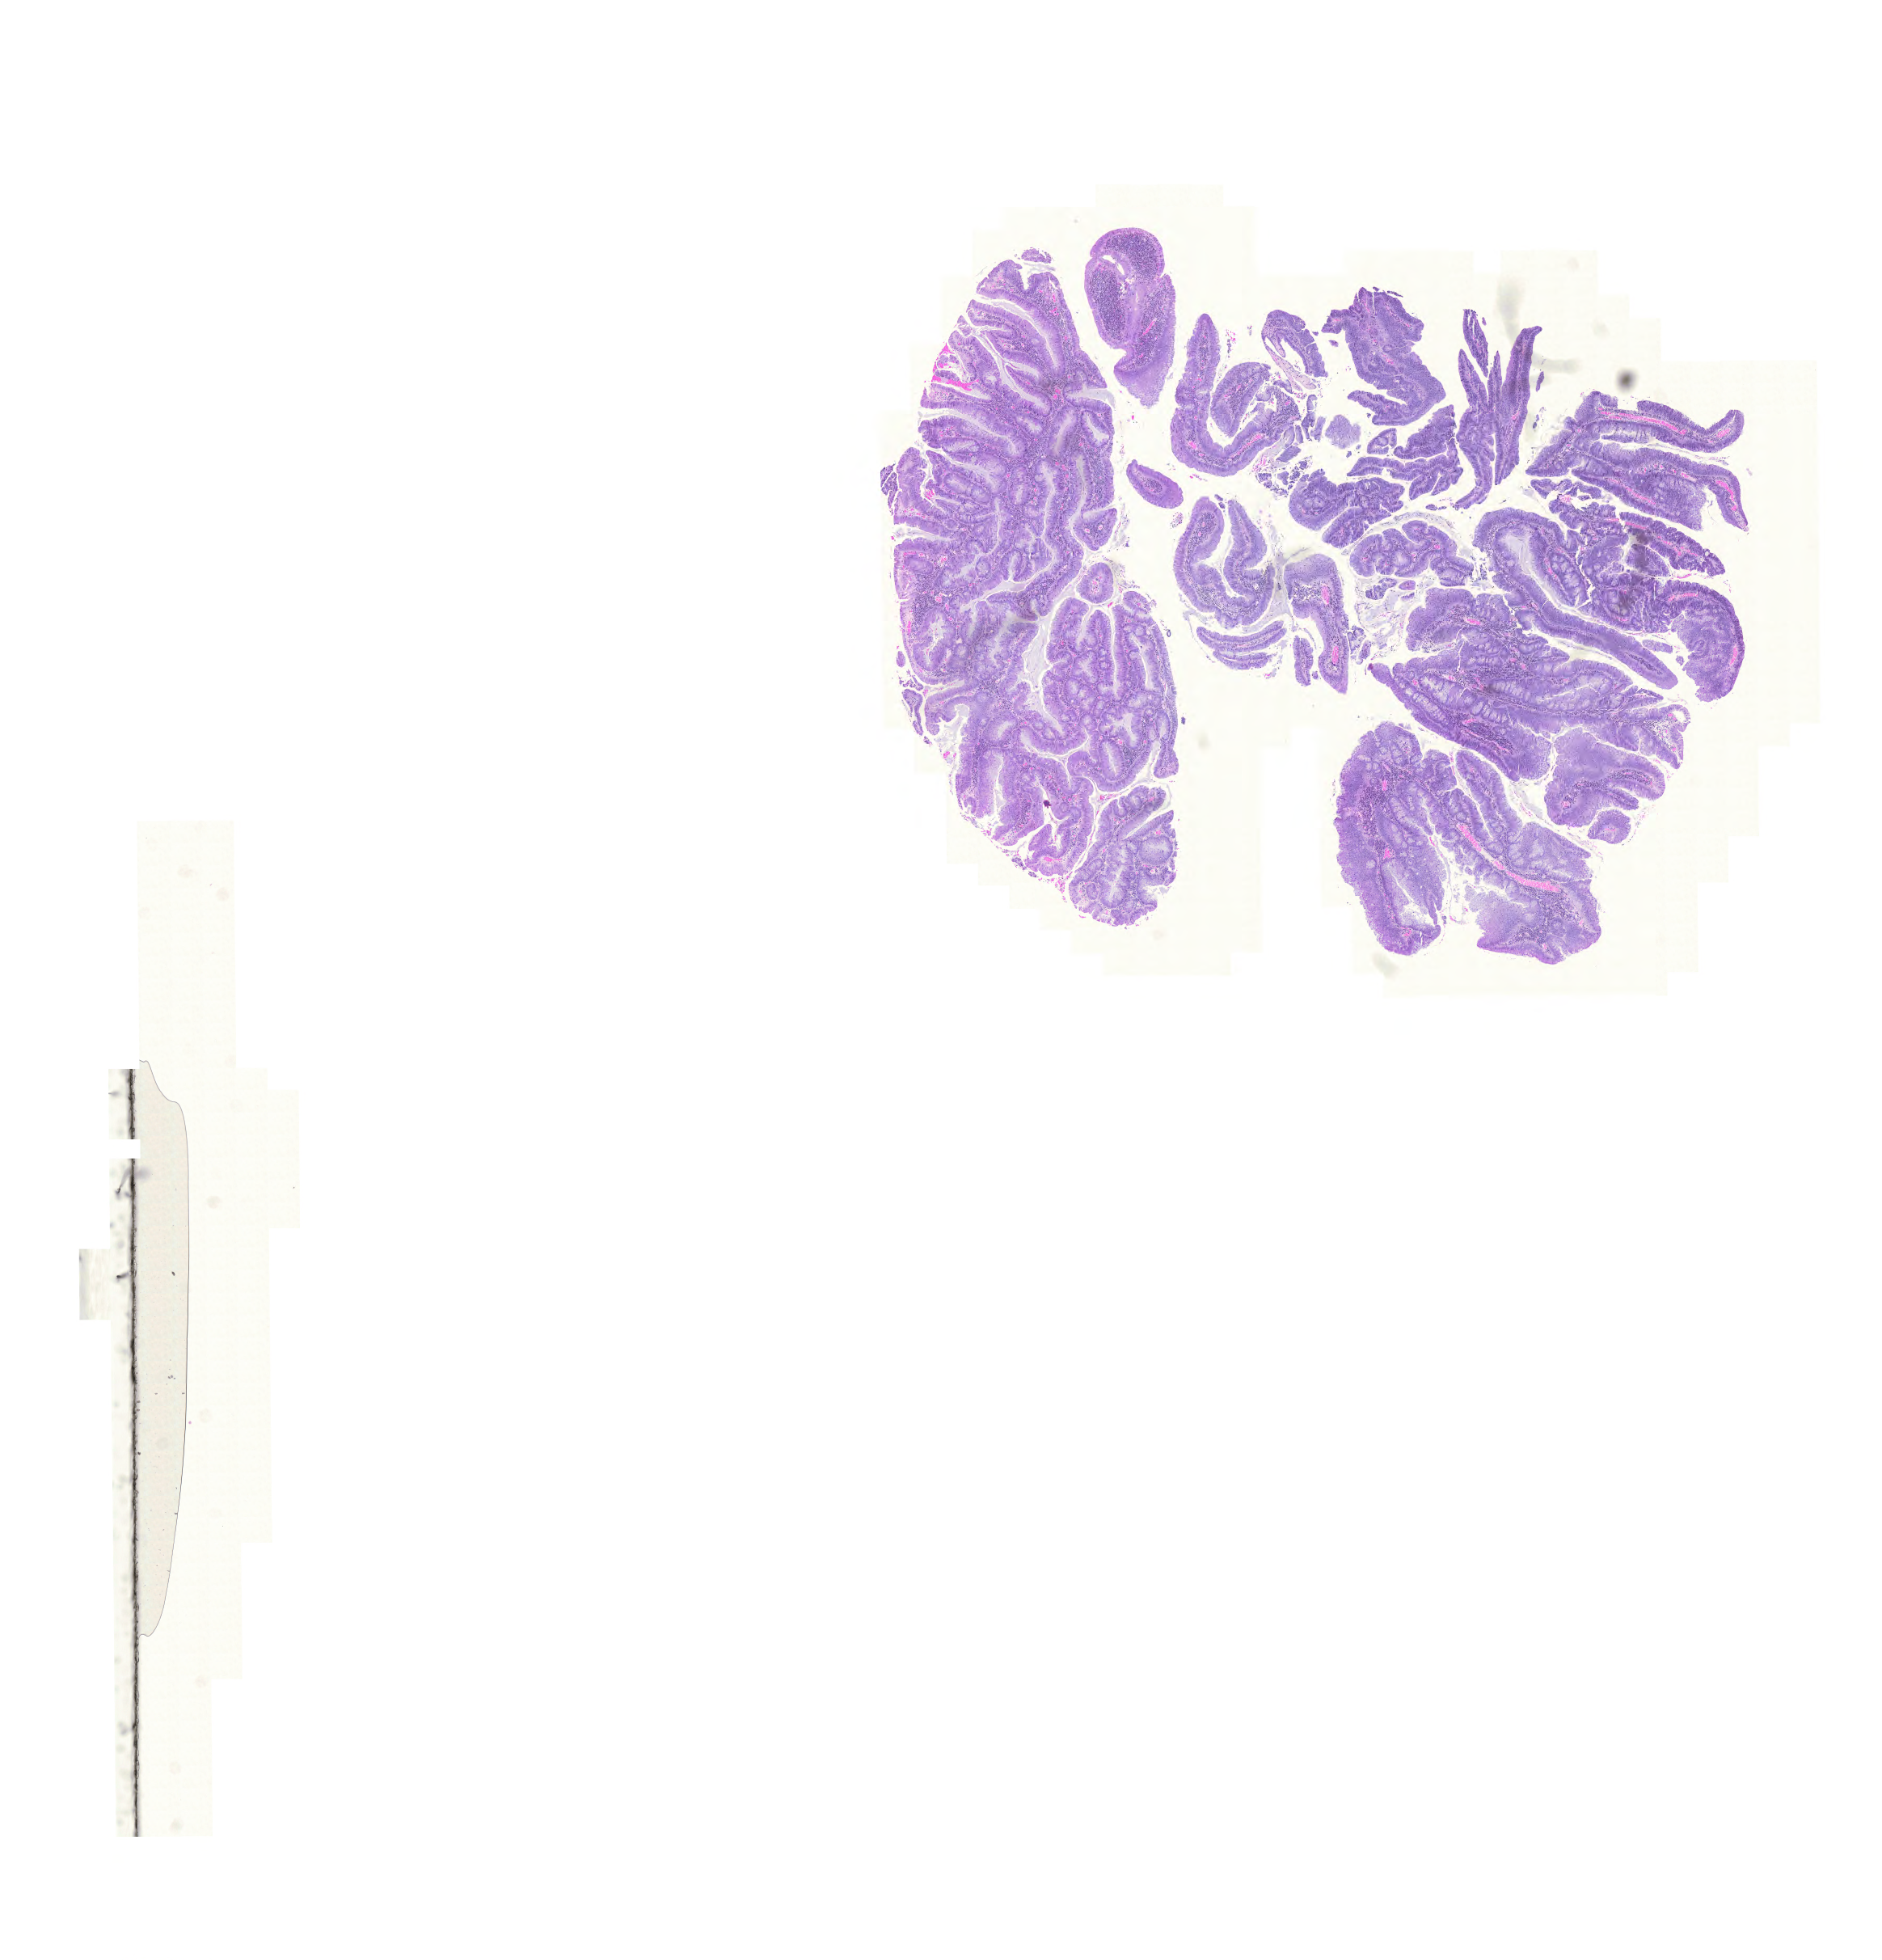
H&E whole-slide image, whole scanned area (about 17.3 x 18.0 mm, slide scanned at 20x) shown as a low-resolution overview; formalin-fixed paraffin-embedded (FFPE) diagnostic section; sample: primary tumour, colon. Patient: male, age at initial diagnosis 72 years.
Diagnosis: Adenocarcinoma, NOS (cecum). AJCC pathologic stage: IIA (6th edition).